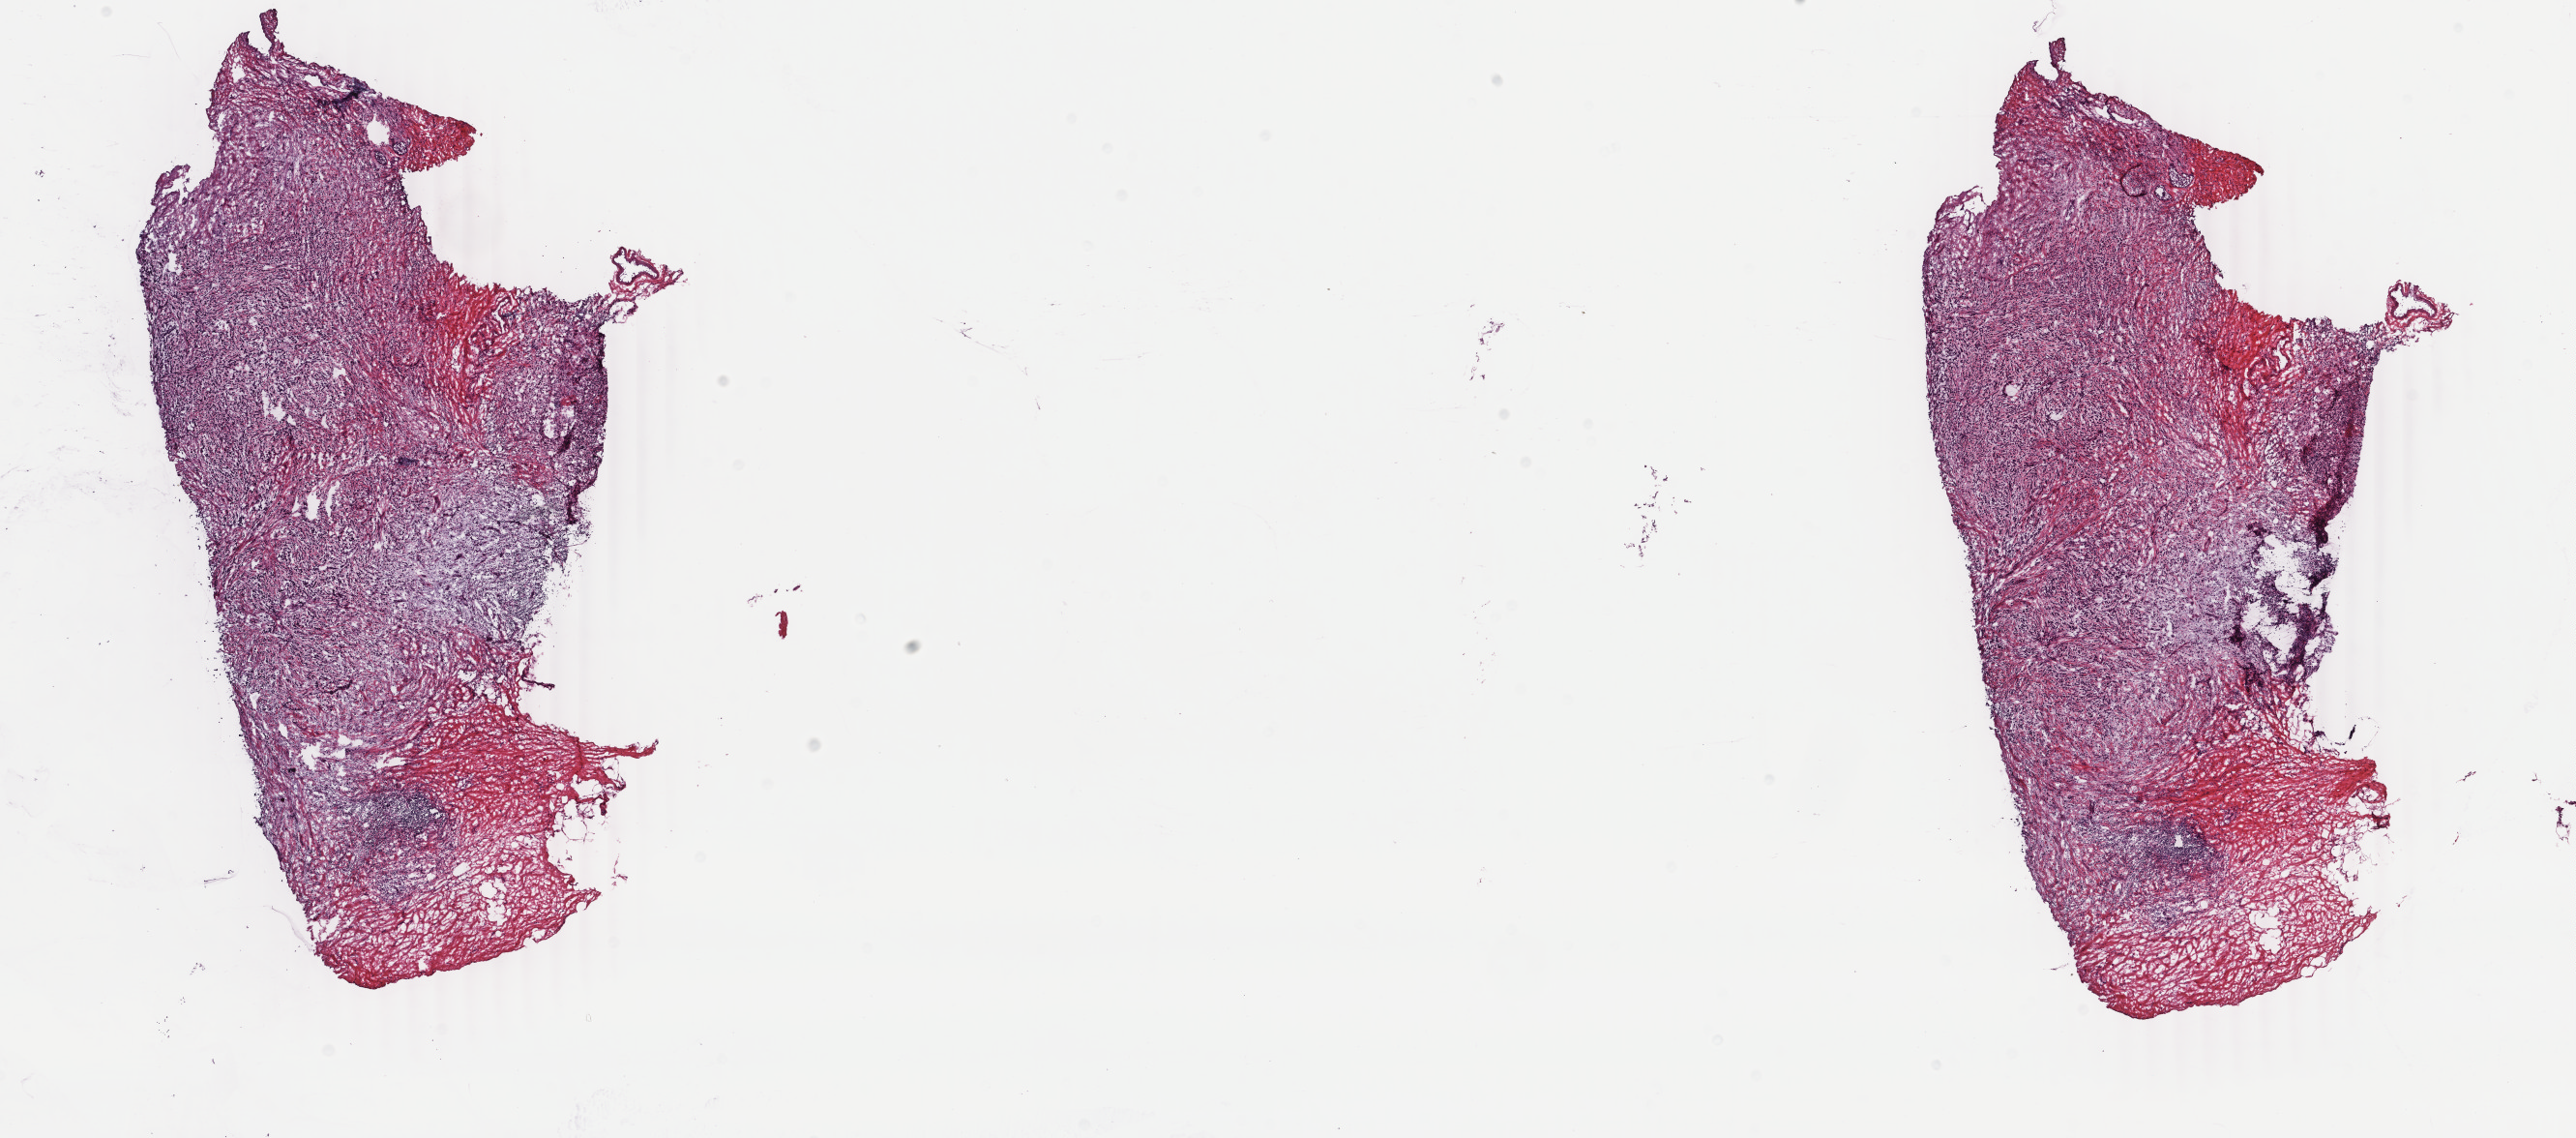
H&E-stained whole-slide image — shown as a low-resolution overview of the whole scanned area (about 21.2 x 9.4 mm, acquisition: 40x scan); frozen section; sample: primary tumour, breast. Patient: female, age at initial diagnosis 41 years. Pathologist review of this section (percent, as recorded): tumour cells 85%, tumour nuclei 90%, normal cells 0%, stromal cells 15%, necrosis 0%. Infiltration values recorded for this section: lymphocyte infiltration 0%, monocyte infiltration 0%, neutrophil infiltration 0%.
Lymph nodes positive (case pathology): 0 of 1 examined. AJCC pathologic stage: IIA. Pathologic diagnosis: Lobular carcinoma, NOS.